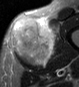
MRI of an extremity soft-tissue mass, one axial slice; position 18 of 45 along the scan axis; STIR; MR volume resampled by the dataset authors to the PET/CT grid (not the native acquisition matrix); 3.27 mm slice thickness; 79 × 87 image matrix, field of view 77 × 85 mm. Male patient. From the clinical record (not read from this slice): histological type: pleiomorphic leiomyosarcoma; grade: high; site of the primary tumour: left thigh.
Structures marked on this image (expert contour drawn on MRI and transferred to this co-registered scan by the dataset authors):
- gross tumour volume including surrounding oedema: box from (x=9, y=16) to (x=60, y=67) px
- gross tumour volume (mass): (x=9, y=16)–(x=55, y=67)